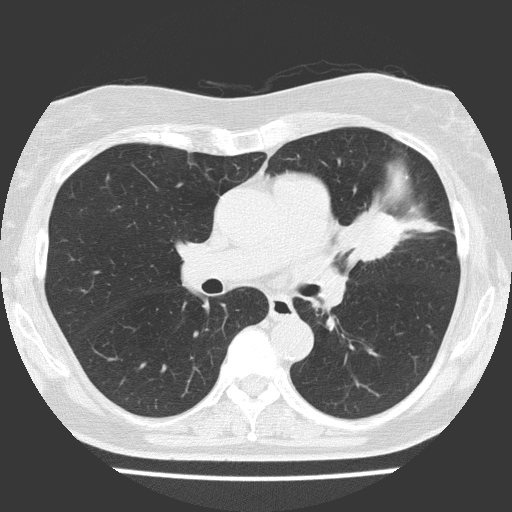
Axial slice from a low-dose chest CT screening exam. Baseline screening round. Lung window (W 1500 / L -600 HU). 2 mm slice thickness. Lung (sharp) reconstruction kernel (FC51). 120 kVp. Slice 68 of 151 in the series. Female participant, aged 70 years at enrolment.
Expert-annotated lung lesion, bounding box <324,186,432,278> (left, top, right, bottom; pixels). The screening reader recorded 2 non-calcified nodules or masses ≥4 mm on this exam (left upper lobe, right upper lobe); which of them this box marks is not recorded. Participant outcome: lung cancer diagnosed 25 days after this screen — adenocarcinoma, NOS, left upper lobe, poorly differentiated (G3), stage IV (AJCC 6th edition), 30 mm at pathology.